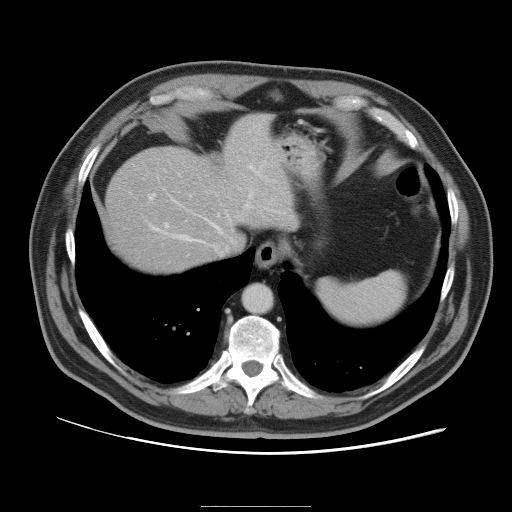
Contrast-enhanced abdominal CT, one axial slice; position 84 of 105 along the scan axis; 120 kVp; intravenous contrast given; soft-tissue window (W 400 / L 40 HU); 512 × 512 image matrix, field of view 399 × 399 mm. Male patient, age 64 years. From the clinical record (not read from this slice): diagnosis: colorectal cancer liver metastases, imaged before liver resection; multiple liver metastases: yes; largest metastasis: 3 cm.
Outlined on this slice (outlined manually by an expert reader):
- hepatic veins: bounding box <149,188,254,243> (left, top, right, bottom; pixels)
- liver: <106,114,292,271>
- planned liver remnant (the part of the liver to remain after resection): <106,153,232,271>
- portal vein (with intrahepatic branches): <148,166,252,235>